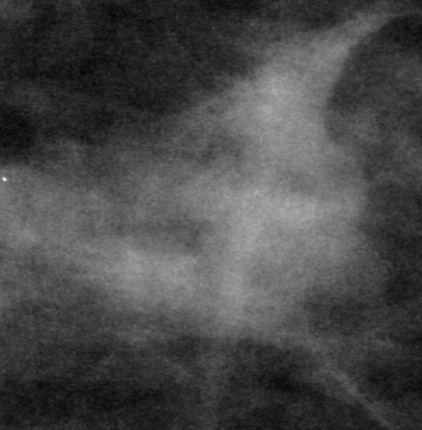
Cropped region of a digitized screen-film mammogram centred on a radiologist-marked abnormality, right breast, CC view, BI-RADS breast density category 2 (scale 1–4).
Mass, shape irregular, margins obscured; BI-RADS assessment category 0; subtlety rating 5 on a 1 (subtle) to 5 (obvious) scale; pathology result (as recorded, not read from the image): benign.